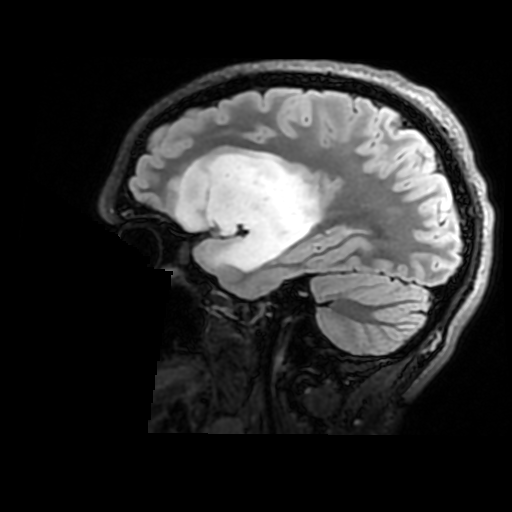
Brain MRI from a brain-tumour surgery series, one sagittal slice; T2 FLAIR; 512 × 512 image matrix, field of view 240 × 240 mm. Case-level facts recorded for this patient, not image findings: histopathology: Astrocytoma; WHO grade: 2; IDH mutation: yes; tumour location: Right Insular.
Annotated regions visible in this slice (outlined manually by an expert reader):
- tumour: bounding box [x1, y1, x2, y2] px = [176, 150, 322, 273]